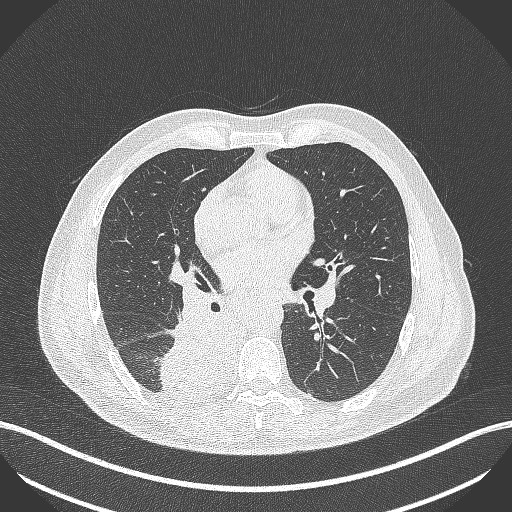
Chest CT, one axial slice; slice 245 of 451 in the series (ordered by position); reconstruction kernel B70f; lung window (W 1500 / L -600 HU); 1 mm slice thickness; 512 × 512 image matrix, field of view 400 × 400 mm. Male patient, age 61 years. Case-level facts recorded for this patient, not image findings: clinical TNM (as recorded): T1 N0 M0.
Outlined on this slice (bounding box drawn by a radiologist):
- lung tumour (recorded histology: small cell carcinoma): box from (x=158, y=306) to (x=239, y=400) px